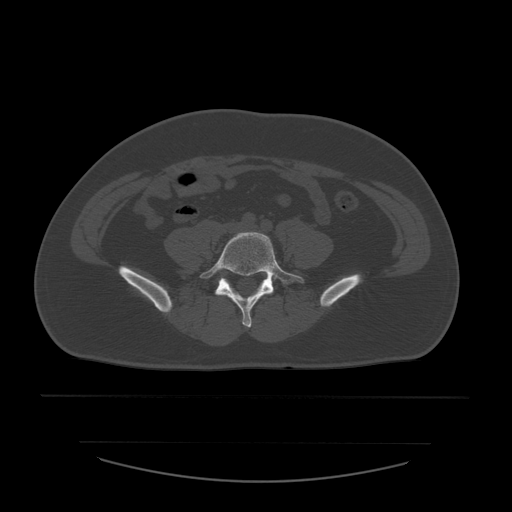
CT including the spine, one axial slice; position 121 of 532 along the scan axis; reconstruction kernel STANDARD; 120 kVp; bone window (W 1800 / L 400 HU); 1.25 mm slice thickness; 512 × 512 image matrix, field of view 441 × 441 mm. Patient age 44 years. From the clinical record (not read from this slice): primary cancer: soft tissue sarcoma.
Annotated regions visible in this slice (semi-automatic segmentation, software-assisted and operator-edited):
- L5 vertebra: bounding box (x1, y1, x2, y2) in pixels: (200, 232, 304, 328)